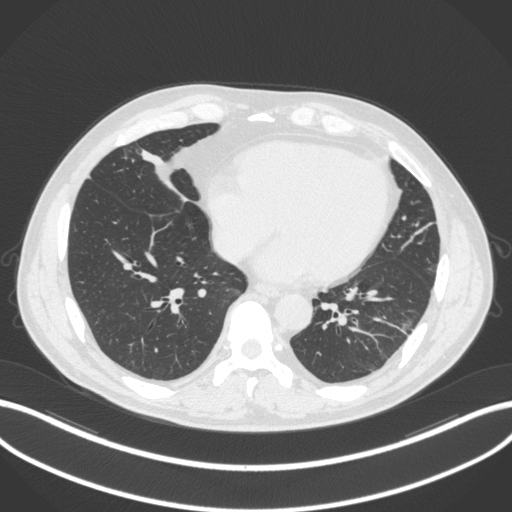
Chest CT, one axial slice. Slice 87 of 399 in the series (ordered by position). Reconstruction kernel B31f. 120 kVp. Lung window (W 1500 / L -600 HU). 1 mm slice thickness. 512 × 512 image matrix. Patient: male, 59 years. Case-level facts recorded for this patient, not image findings: clinical TNM (as recorded): T2a N1 M0.
Annotated regions visible in this slice (bounding box drawn by a radiologist):
- lung tumour (recorded histology: adenocarcinoma): bounding box [x1, y1, x2, y2] px = [135, 143, 176, 183]